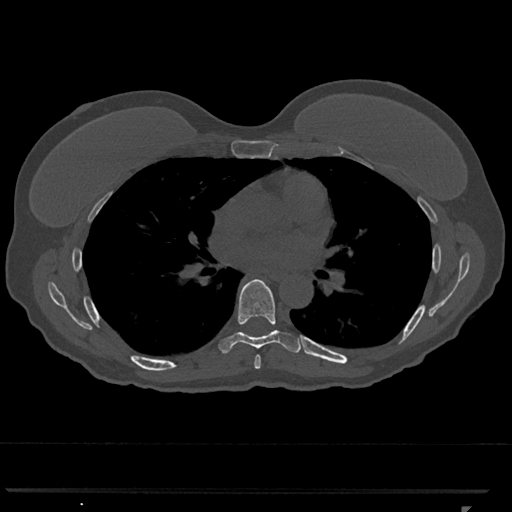
CT including the spine, one axial slice; slice 716 of 793 in the series (ordered by position); reconstruction kernel Br40s/3; bone window (W 1800 / L 400 HU); 512 × 512 image matrix, field of view 380 × 380 mm. Female patient, age 62 years. From the clinical record (not read from this slice): primary cancer: renal.
Structures marked on this image (semi-automatic segmentation, software-assisted and operator-edited):
- T6 vertebra: bounding box (x1, y1, x2, y2) in pixels: (254, 355, 261, 369)
- T7 vertebra: (219, 279, 301, 354)